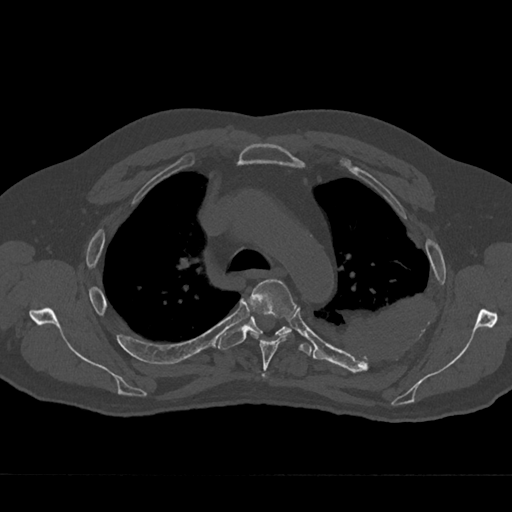
CT including the spine, one axial slice. Position 501 of 797 along the scan axis. Reconstruction kernel Br40s/3. Bone window (W 1800 / L 400 HU). 512 × 512 image matrix, field of view 377 × 377 mm. Male patient, age 75 years. From the clinical record (not read from this slice): primary cancer: renal.
Outlined on this slice (semi-automatically segmented with operator editing):
- T4 vertebra: bounding box [x1, y1, x2, y2] px = [248, 279, 295, 379]
- T5 vertebra: [219, 316, 312, 356]